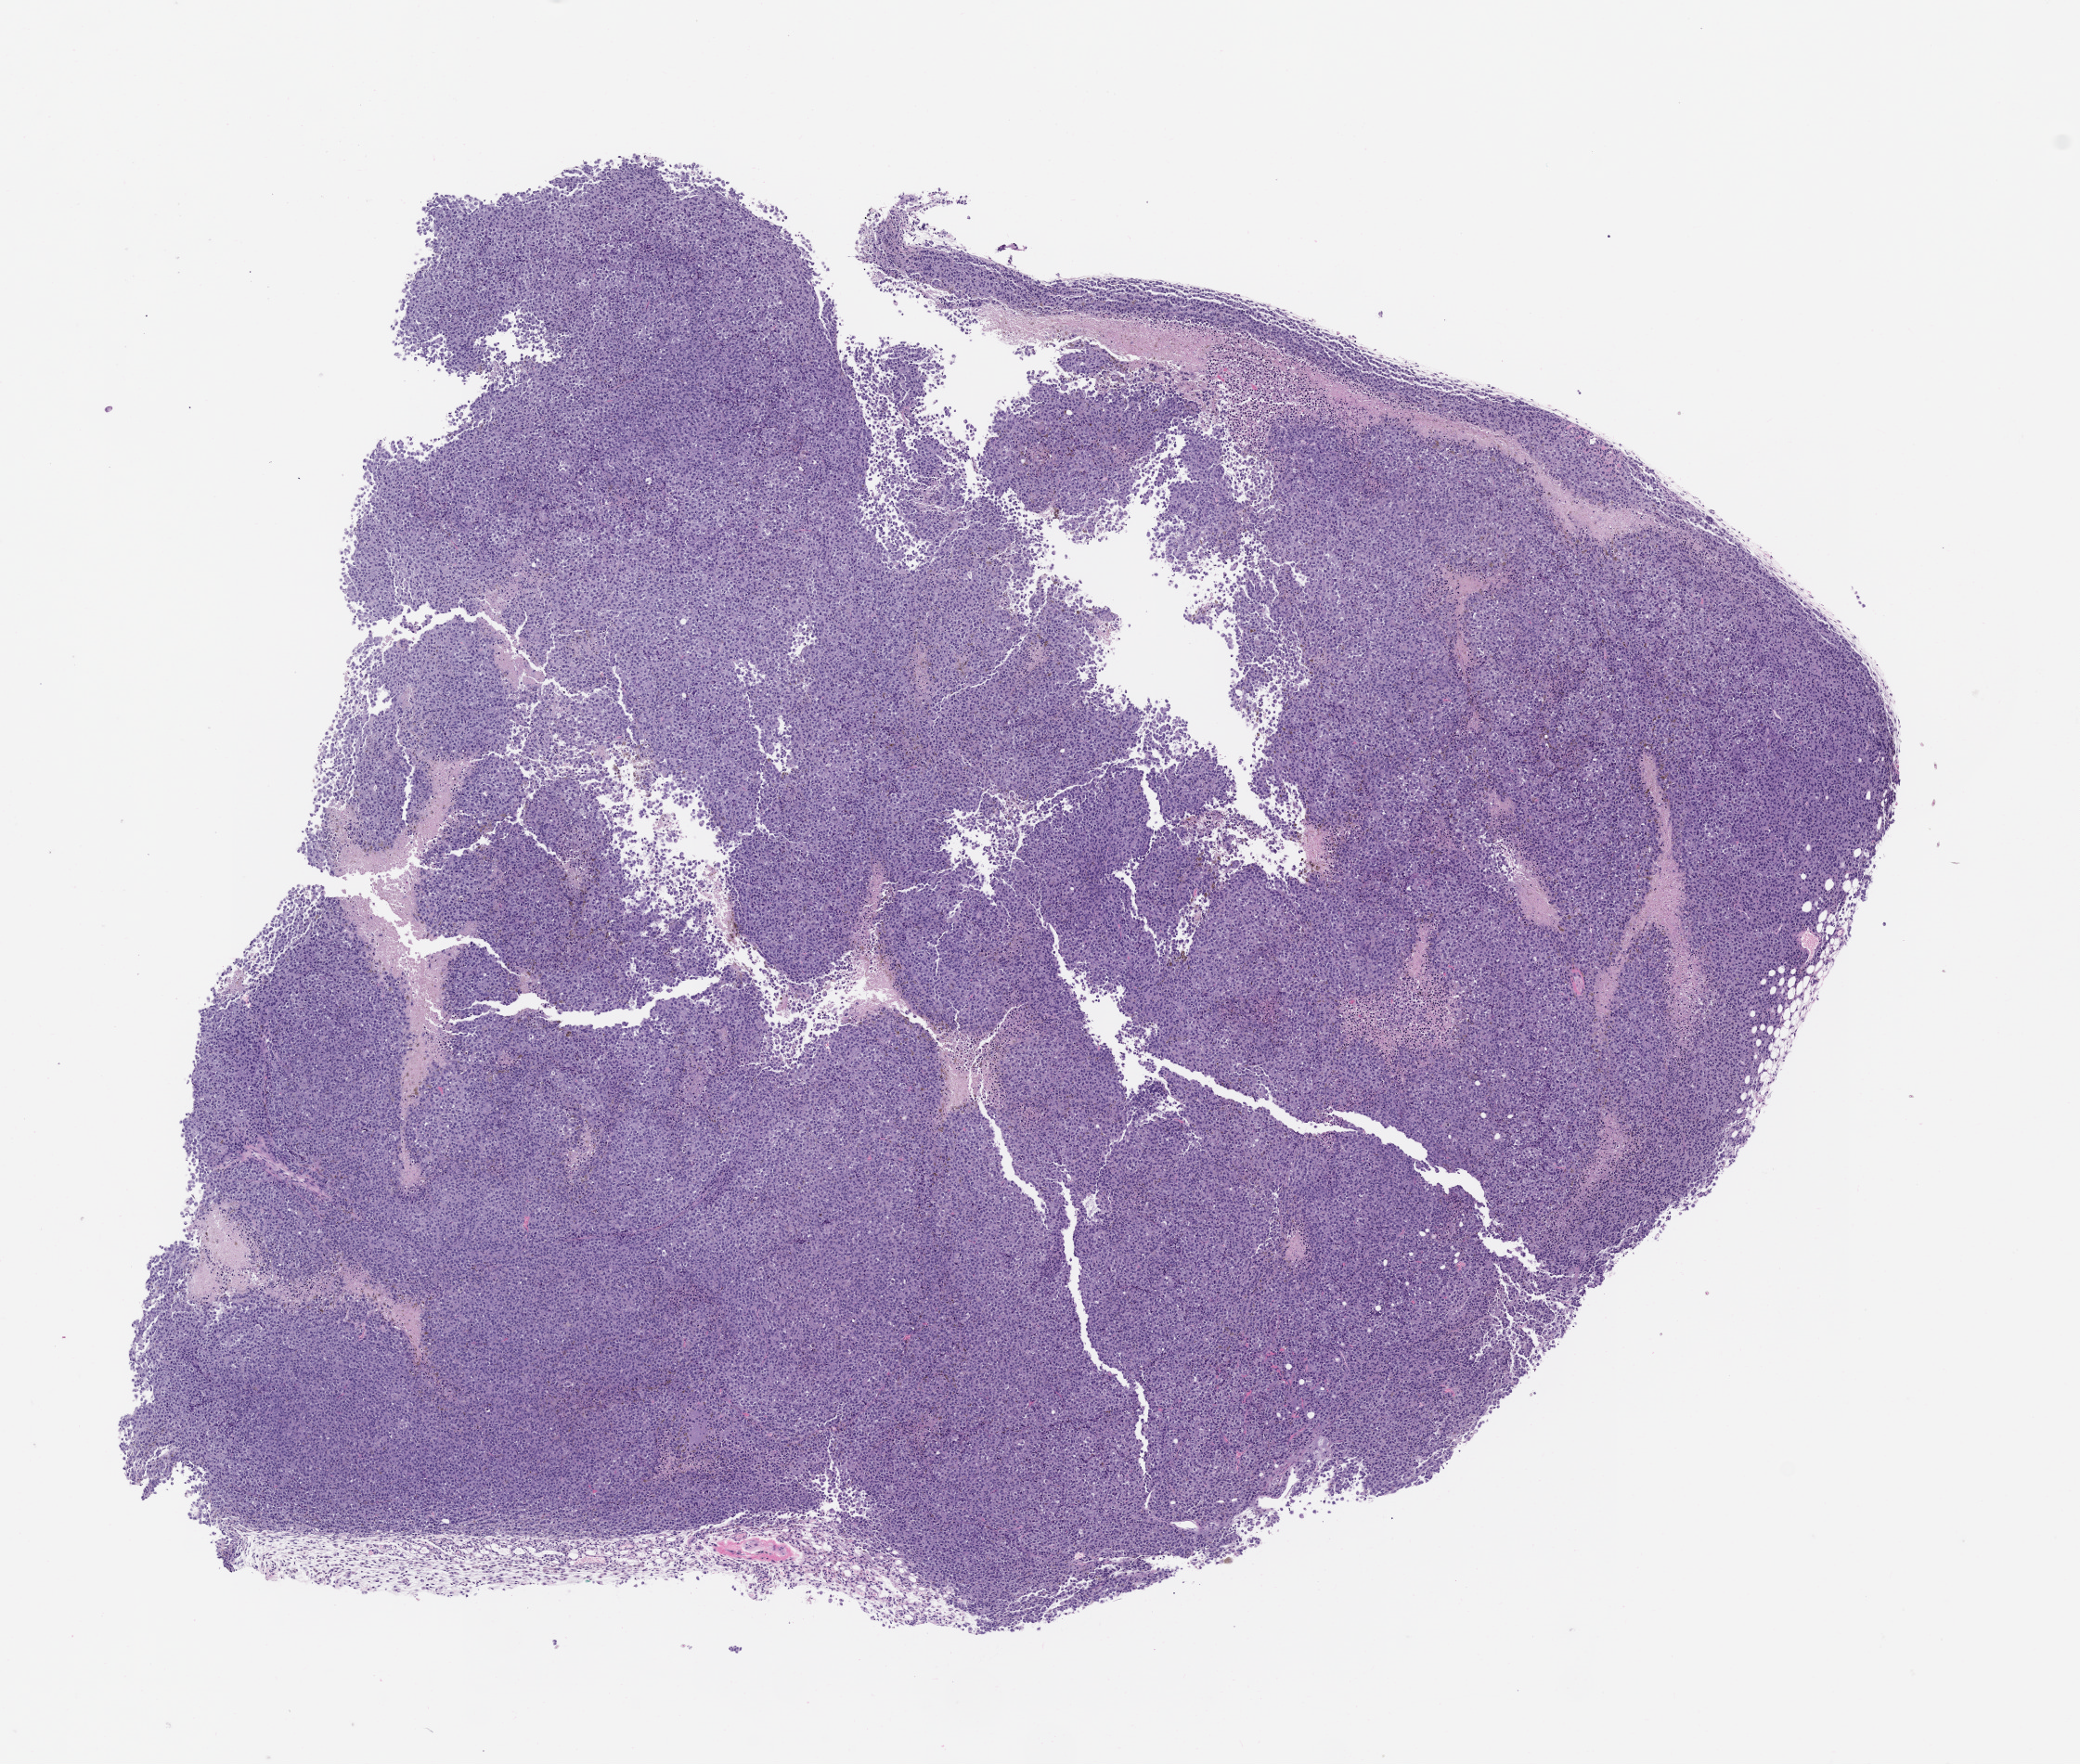
Whole-slide image, hematoxylin and eosin (H&E): patient-derived xenograft (human tumor grown in a mouse), passage 2, shown as a low-resolution overview of the whole scanned area (about 9.0 x 7.6 mm). Formalin-fixed, paraffin-embedded (FFPE) tissue. Originating tumor site category: skin.
Originating patient diagnosis: Melanoma.